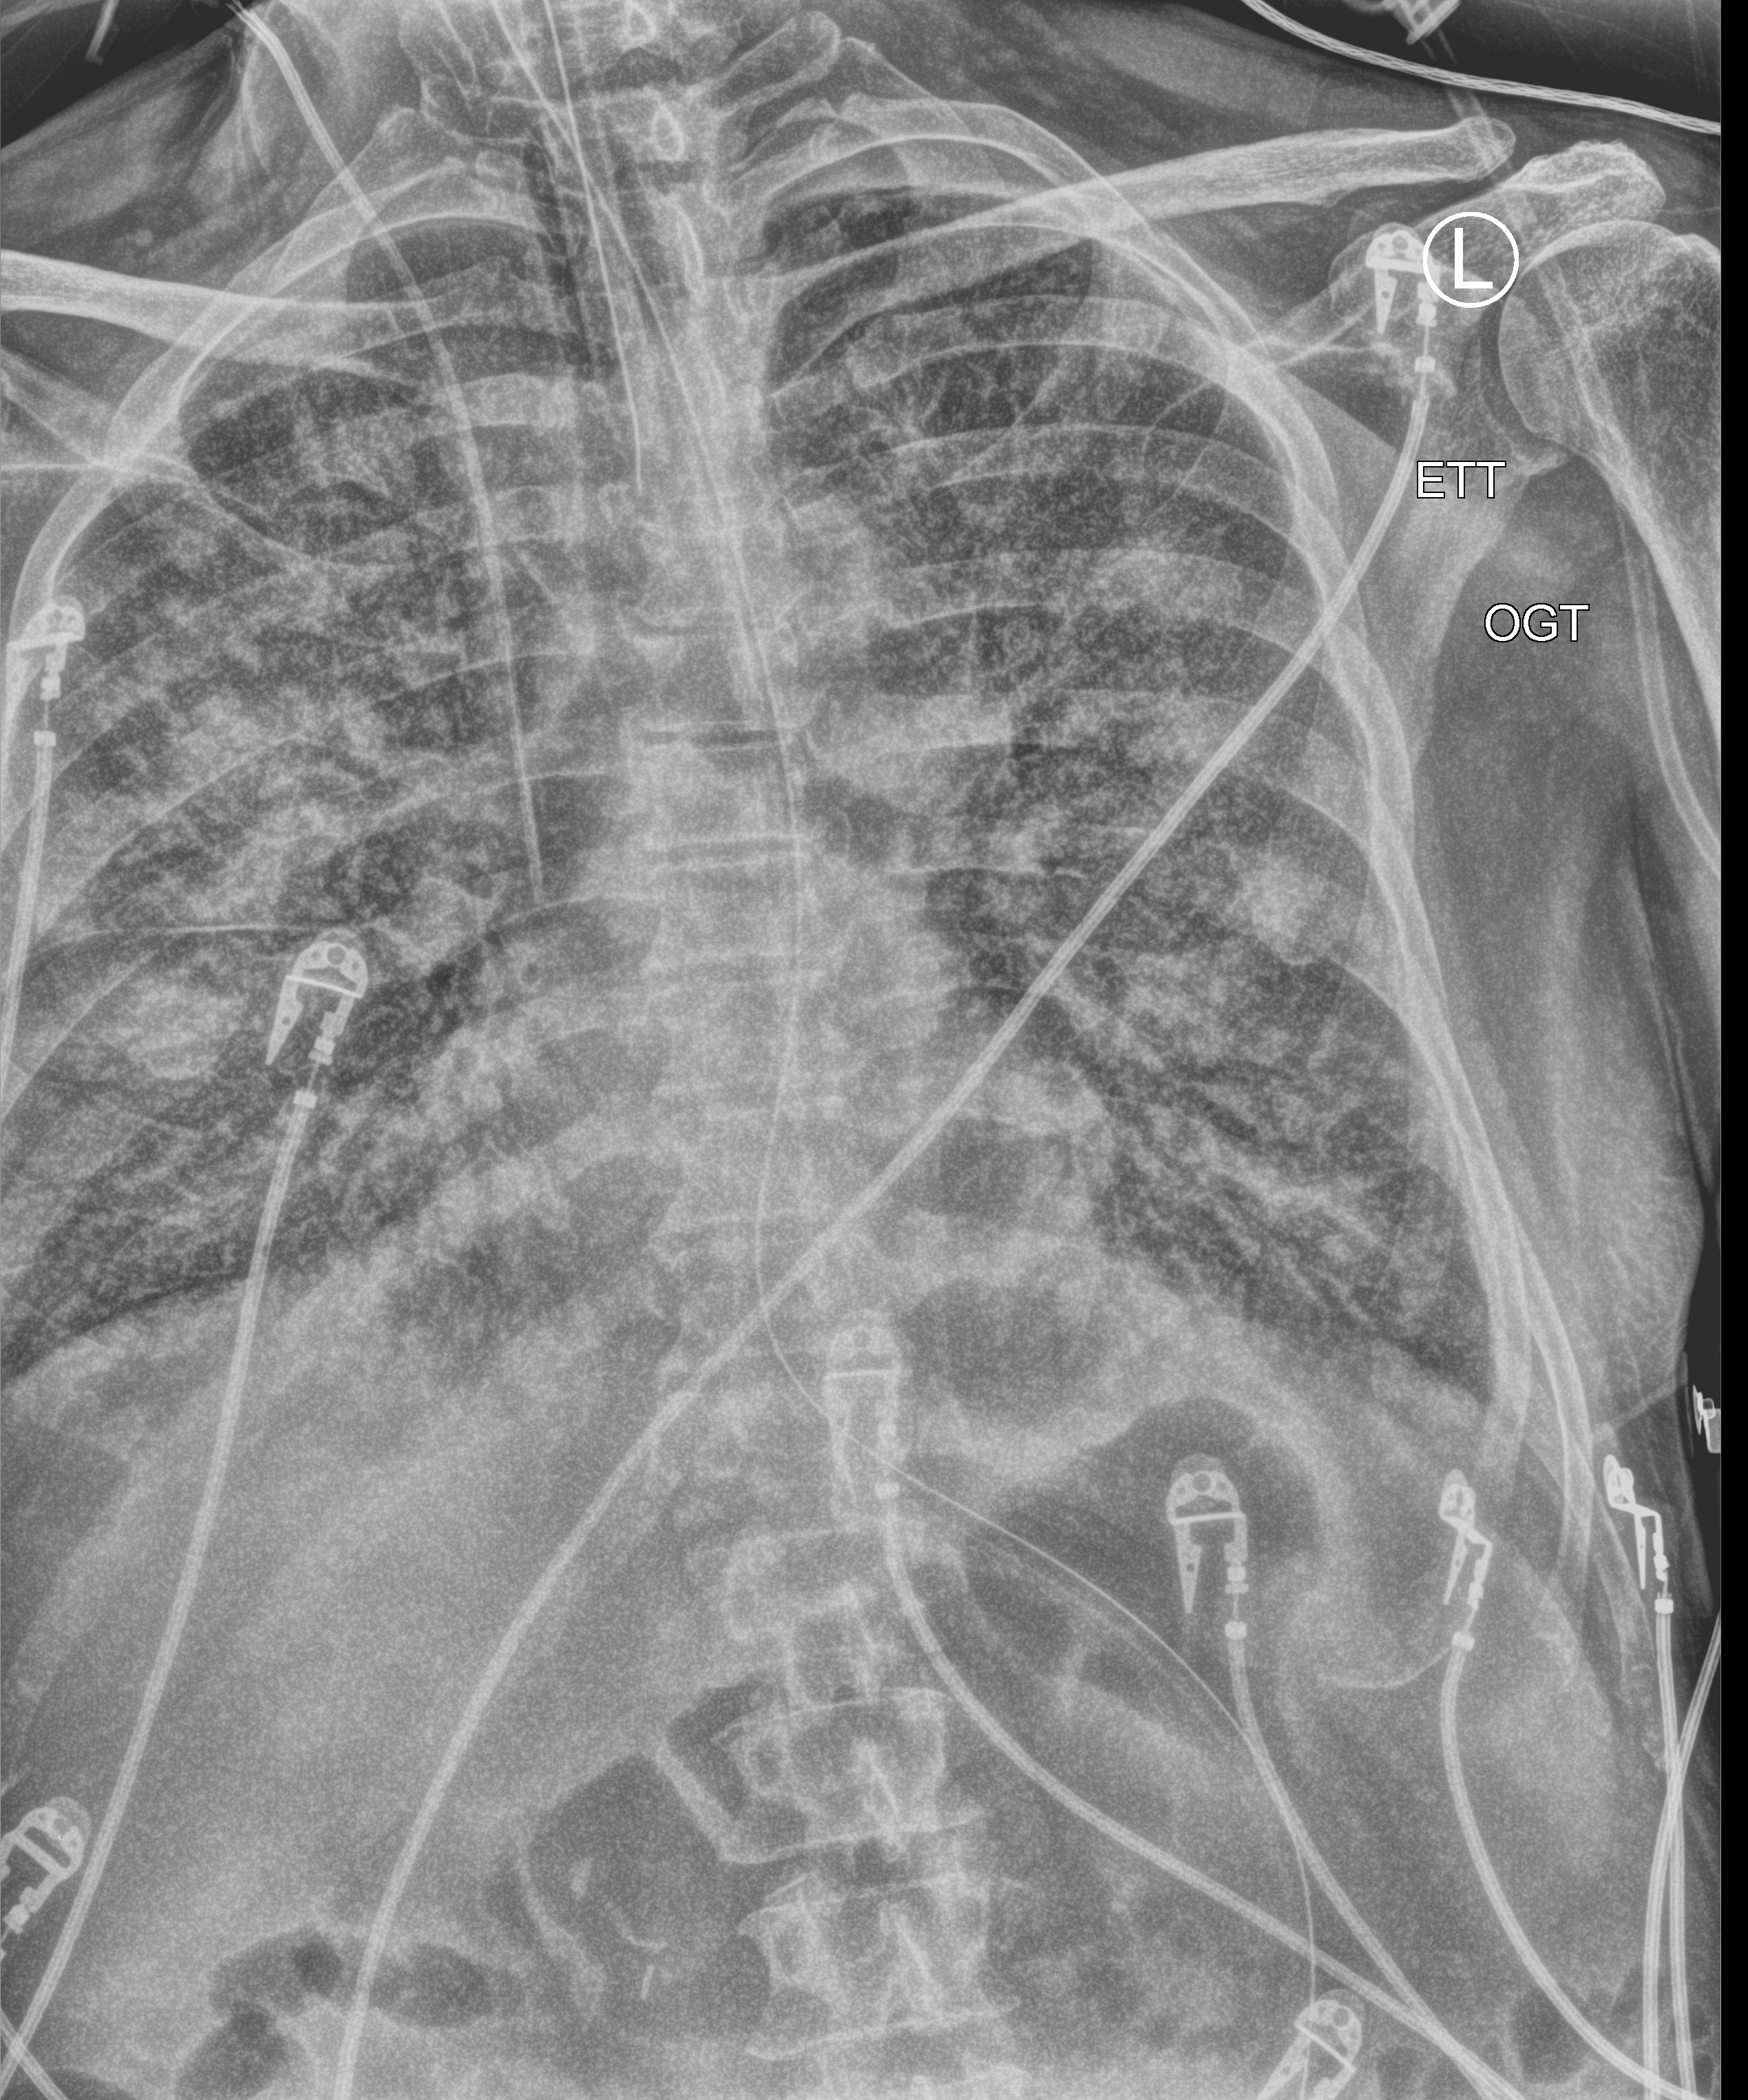
Bedside chest radiograph (computed radiography); anteroposterior (AP) projection. Patient hospitalised with COVID-19; male, aged 60–74 years.
From the hospital-stay record, not from the radiograph (when in the stay this image was taken is not recorded):
- smoking status (admission record): former
- hypertension (admission record): no
- mechanically ventilated during this hospital stay: yes